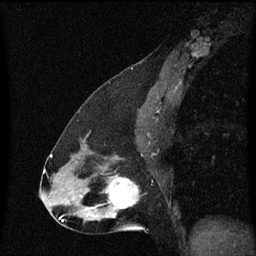
Breast MRI (dynamic contrast-enhanced), one sagittal slice; slice 34 of 60 in the series (ordered by position); dynamic contrast-enhanced series, image 2 of 3 at this slice position (ordered by acquisition); 1.5 T; TE 4.2 ms, TR 8.4 ms; 2 mm slice thickness; 256 × 256 image matrix, field of view 200 × 200 mm. Female patient, age 47 years.
Outlined on this slice (semi-automatic segmentation, software-assisted and operator-edited):
- analysis volume of interest (the breast-tissue region the enhancement analysis was run in; not a lesion): bounding box [x1, y1, x2, y2] px = [100, 172, 140, 219]
- tumour enhancement mask (voxels above the 70 % enhancement threshold inside the analysis volume of interest): [107, 176, 139, 211]